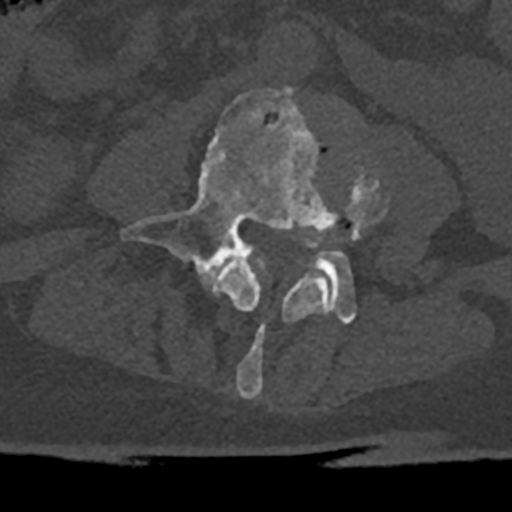
CT including the spine, one axial slice; position 282 of 797 along the scan axis; reconstruction kernel Br40s/3; 120 kVp; bone window (W 1800 / L 400 HU); 512 × 512 image matrix, field of view 160 × 160 mm. Male patient, age 74 years. Case-level facts recorded for this patient, not image findings: primary cancer: renal; vertebrae with lytic lesions (as recorded): T10, L1, L2, L3, L4, L5.
Outlined on this slice (semi-automatically segmented with operator editing):
- L3 vertebra: box from (x=214, y=163) to (x=386, y=398) px
- L4 vertebra: (x=121, y=89)–(x=356, y=324)